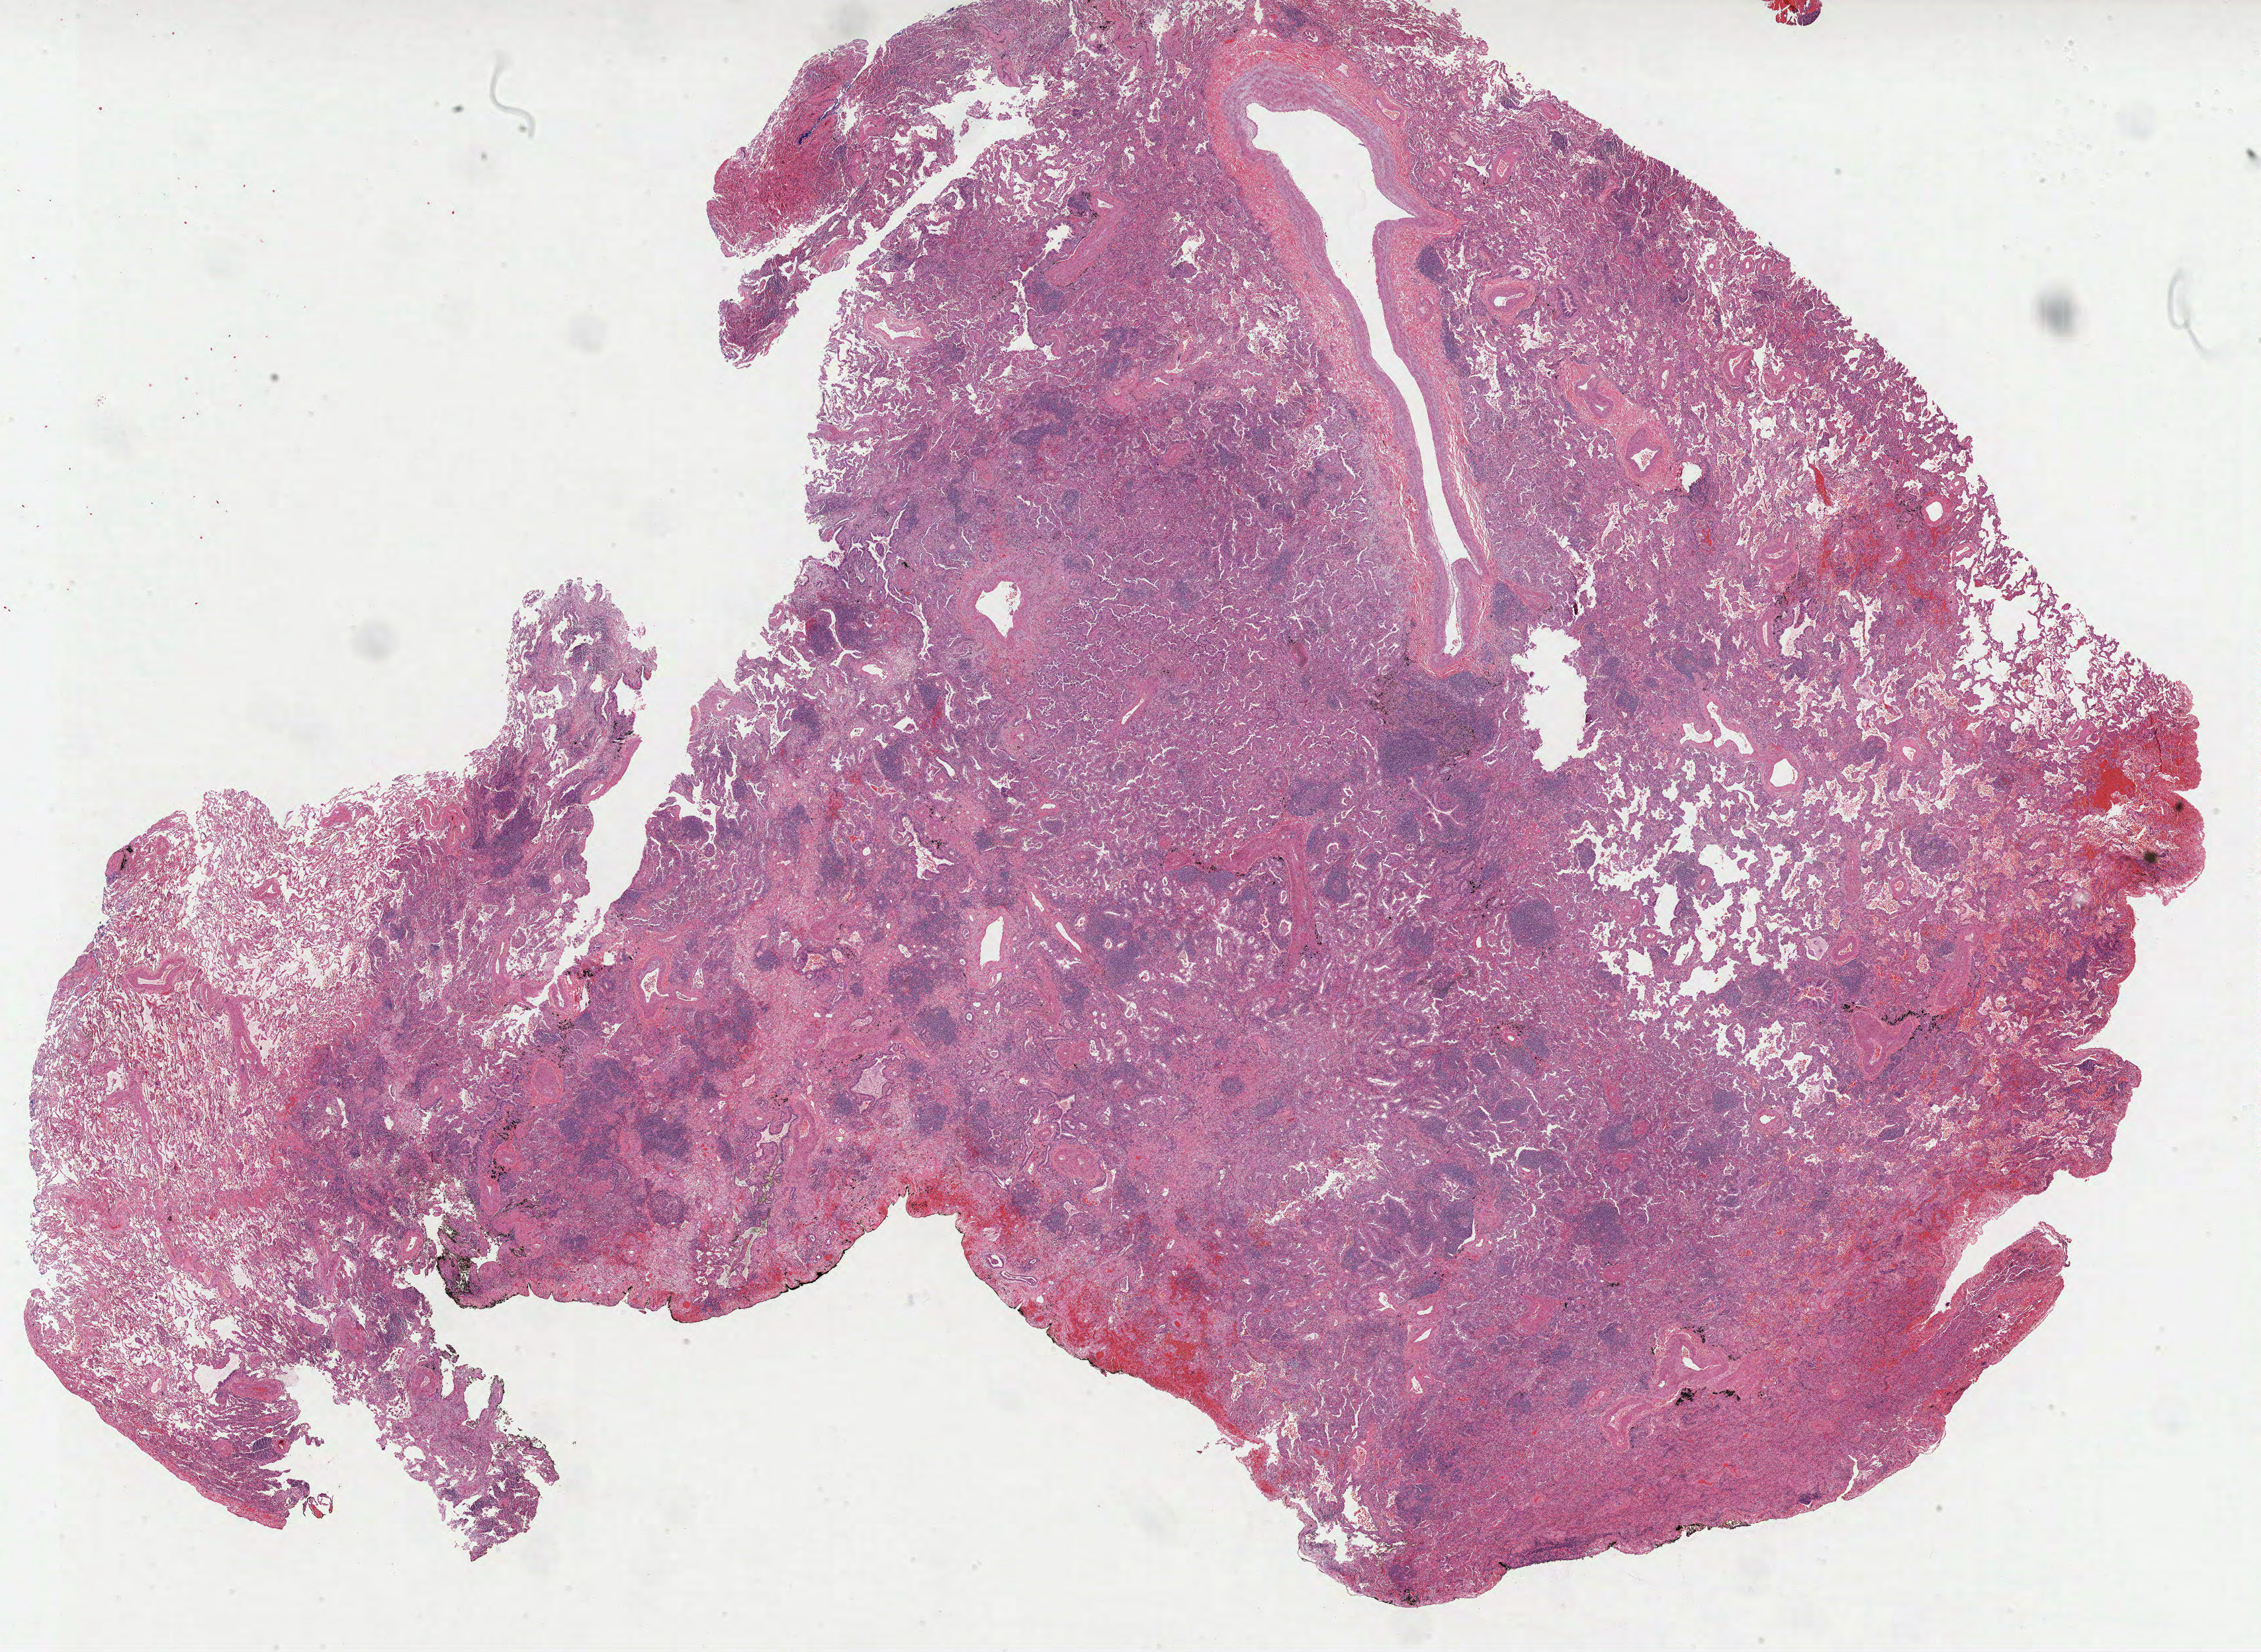
H&E whole-slide image — whole scanned area (about 27.6 x 20.1 mm) shown as a low-resolution overview; formalin-fixed paraffin-embedded (FFPE) diagnostic section; lung, primary tumour sample. Female patient; age at initial diagnosis 79 years.
Diagnosis: Adenocarcinoma with mixed subtypes (lower lobe, lung). AJCC pathologic stage: IIA (6th edition).